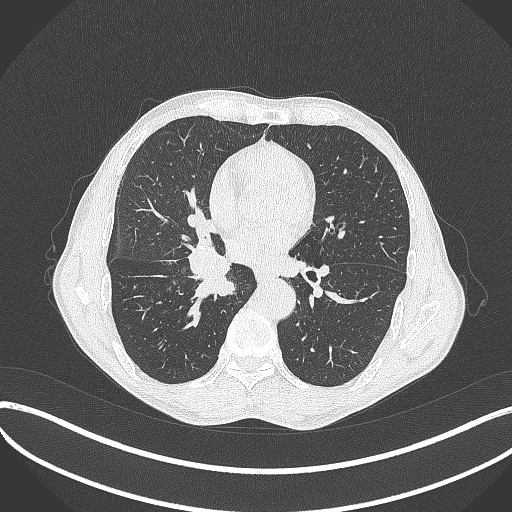
Chest CT, one axial slice; position 205 of 481 along the scan axis; reconstruction kernel B70f; lung window (W 1500 / L -600 HU); 1 mm slice thickness; 512 × 512 image matrix, field of view 400 × 400 mm. Male patient, age 65 years. From the clinical record (not read from this slice): clinical TNM (as recorded): T2a N0 M0.
Outlined on this slice (bounding box drawn by a radiologist):
- lung tumour (recorded histology: squamous cell carcinoma): bounding box (x1, y1, x2, y2) in pixels: (183, 240, 240, 301)